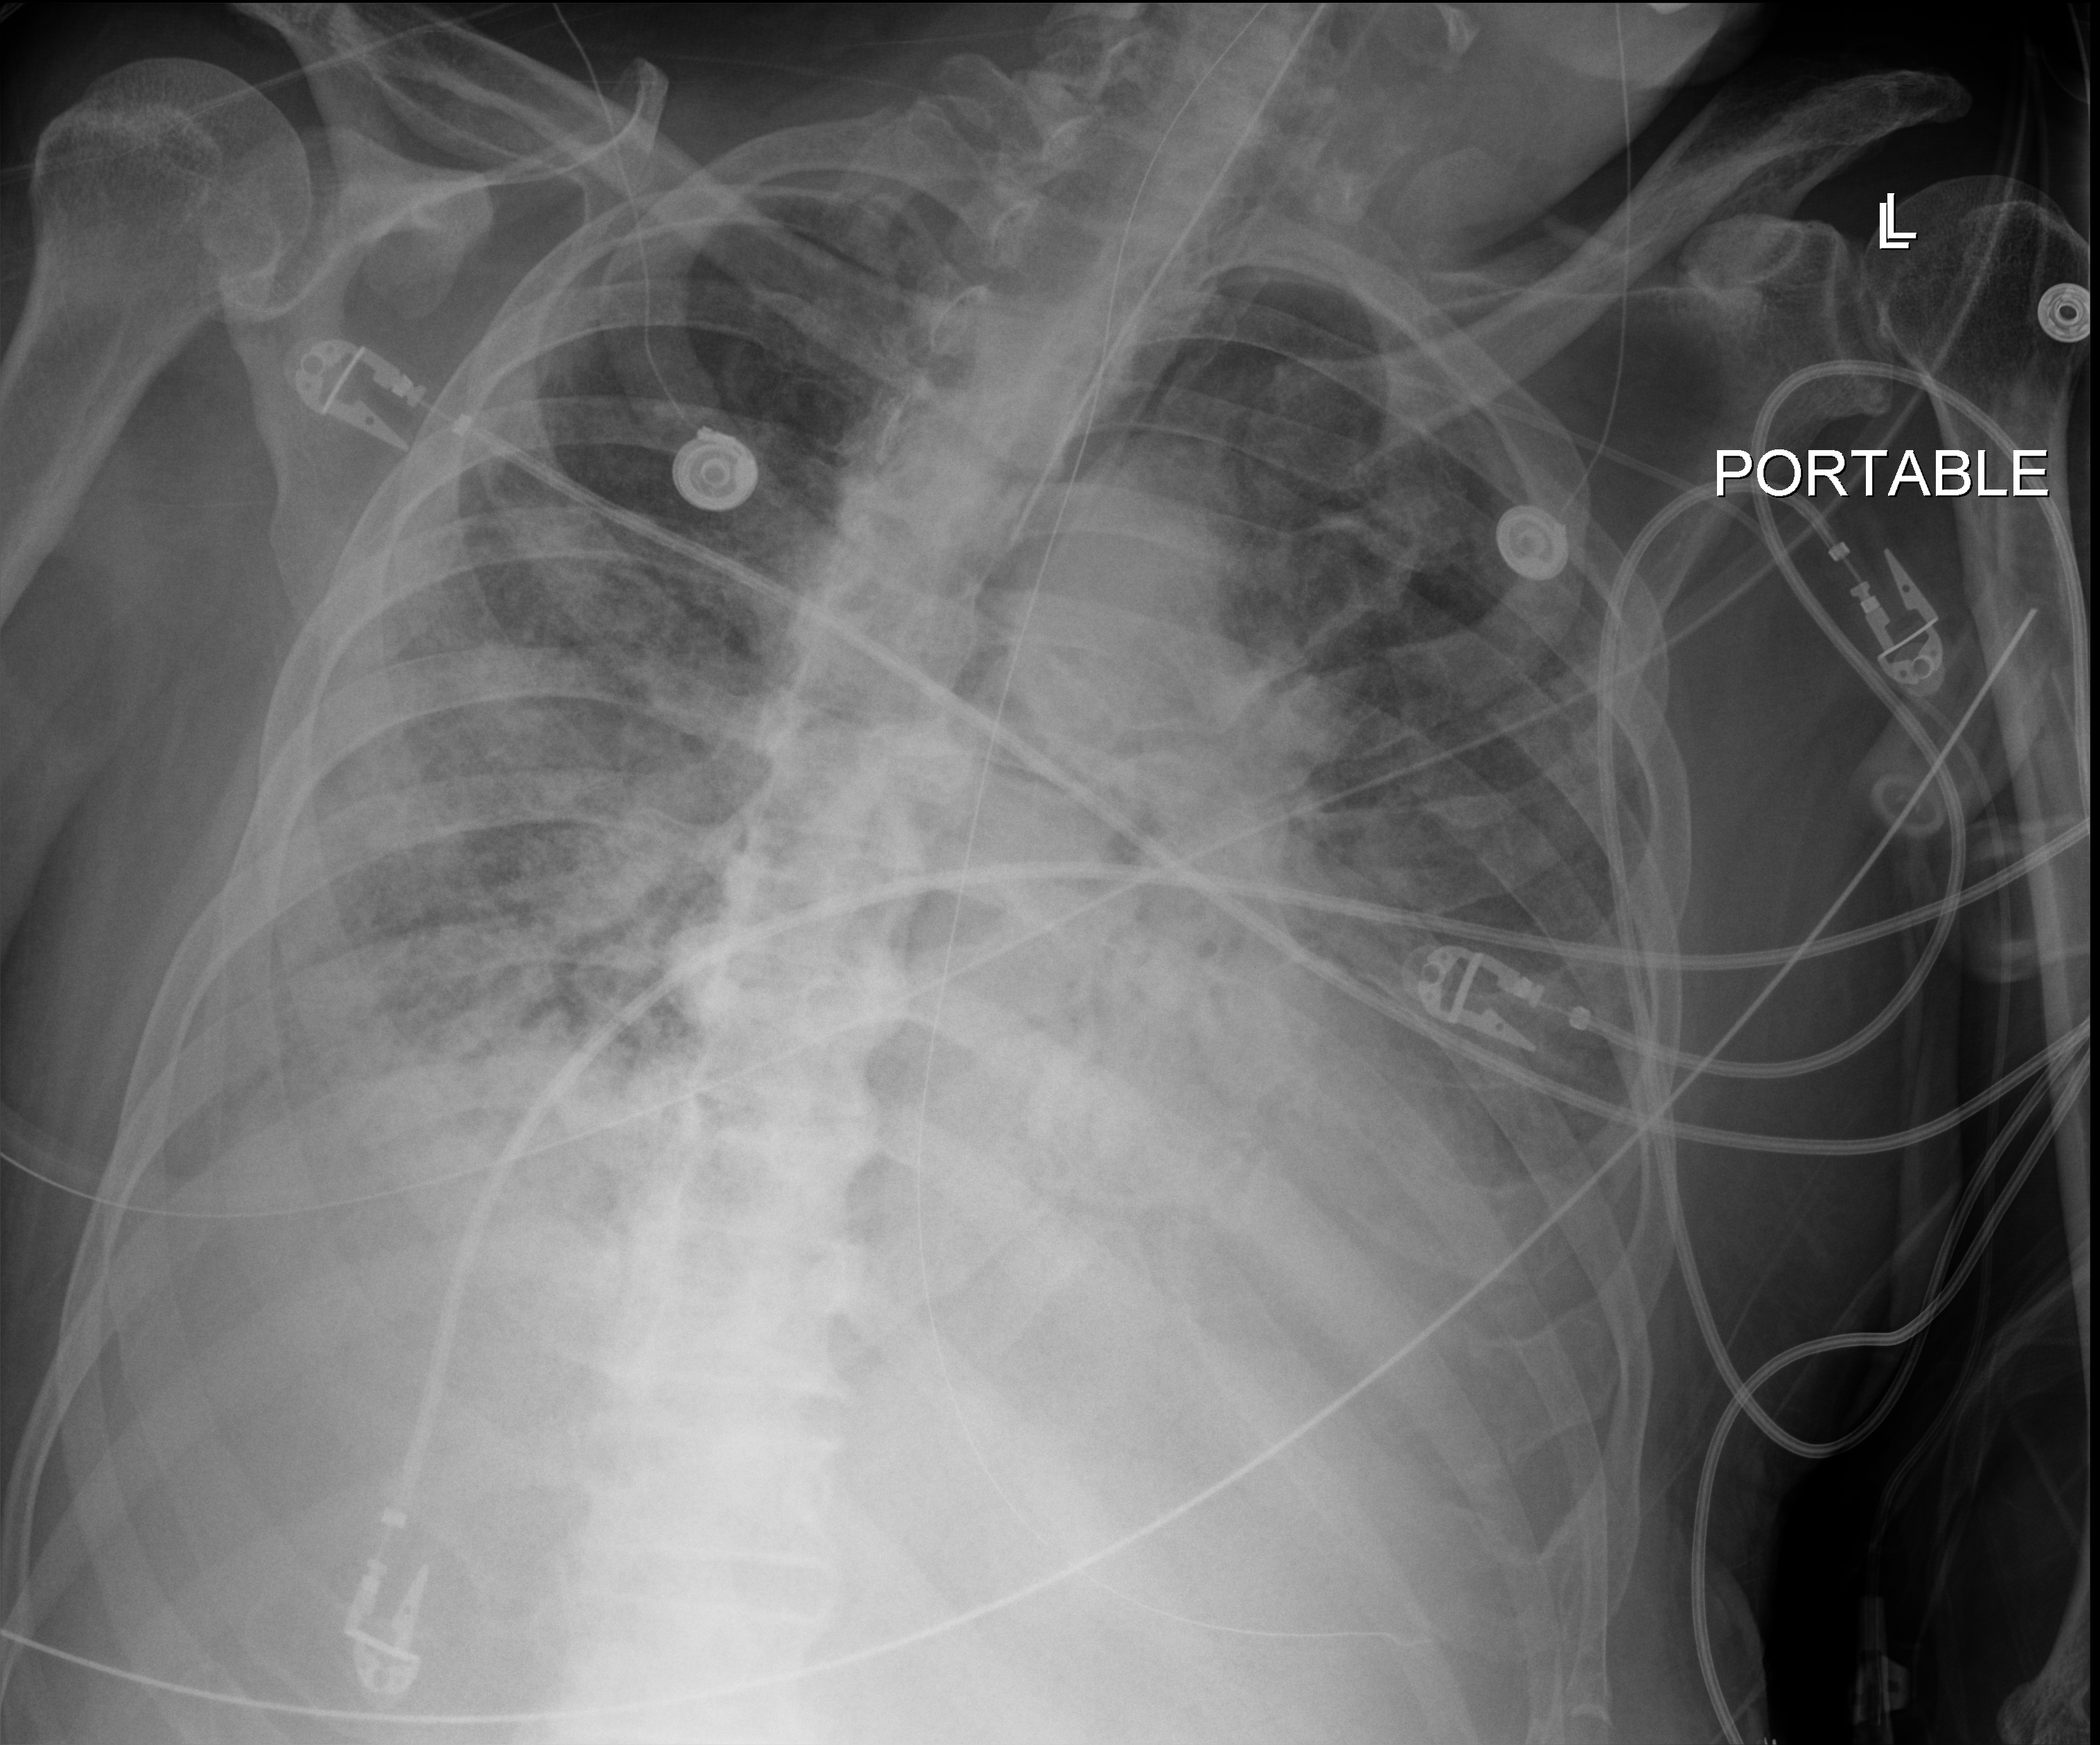
Chest X-ray (portable). Patient hospitalised with COVID-19; male, aged 75–90 years.
Hospital-stay facts (about this admission, not read from this image; timing relative to this image not recorded): mechanically ventilated during this hospital stay: yes; admitted to intensive care during this hospital stay: yes; COPD (admission record): no.